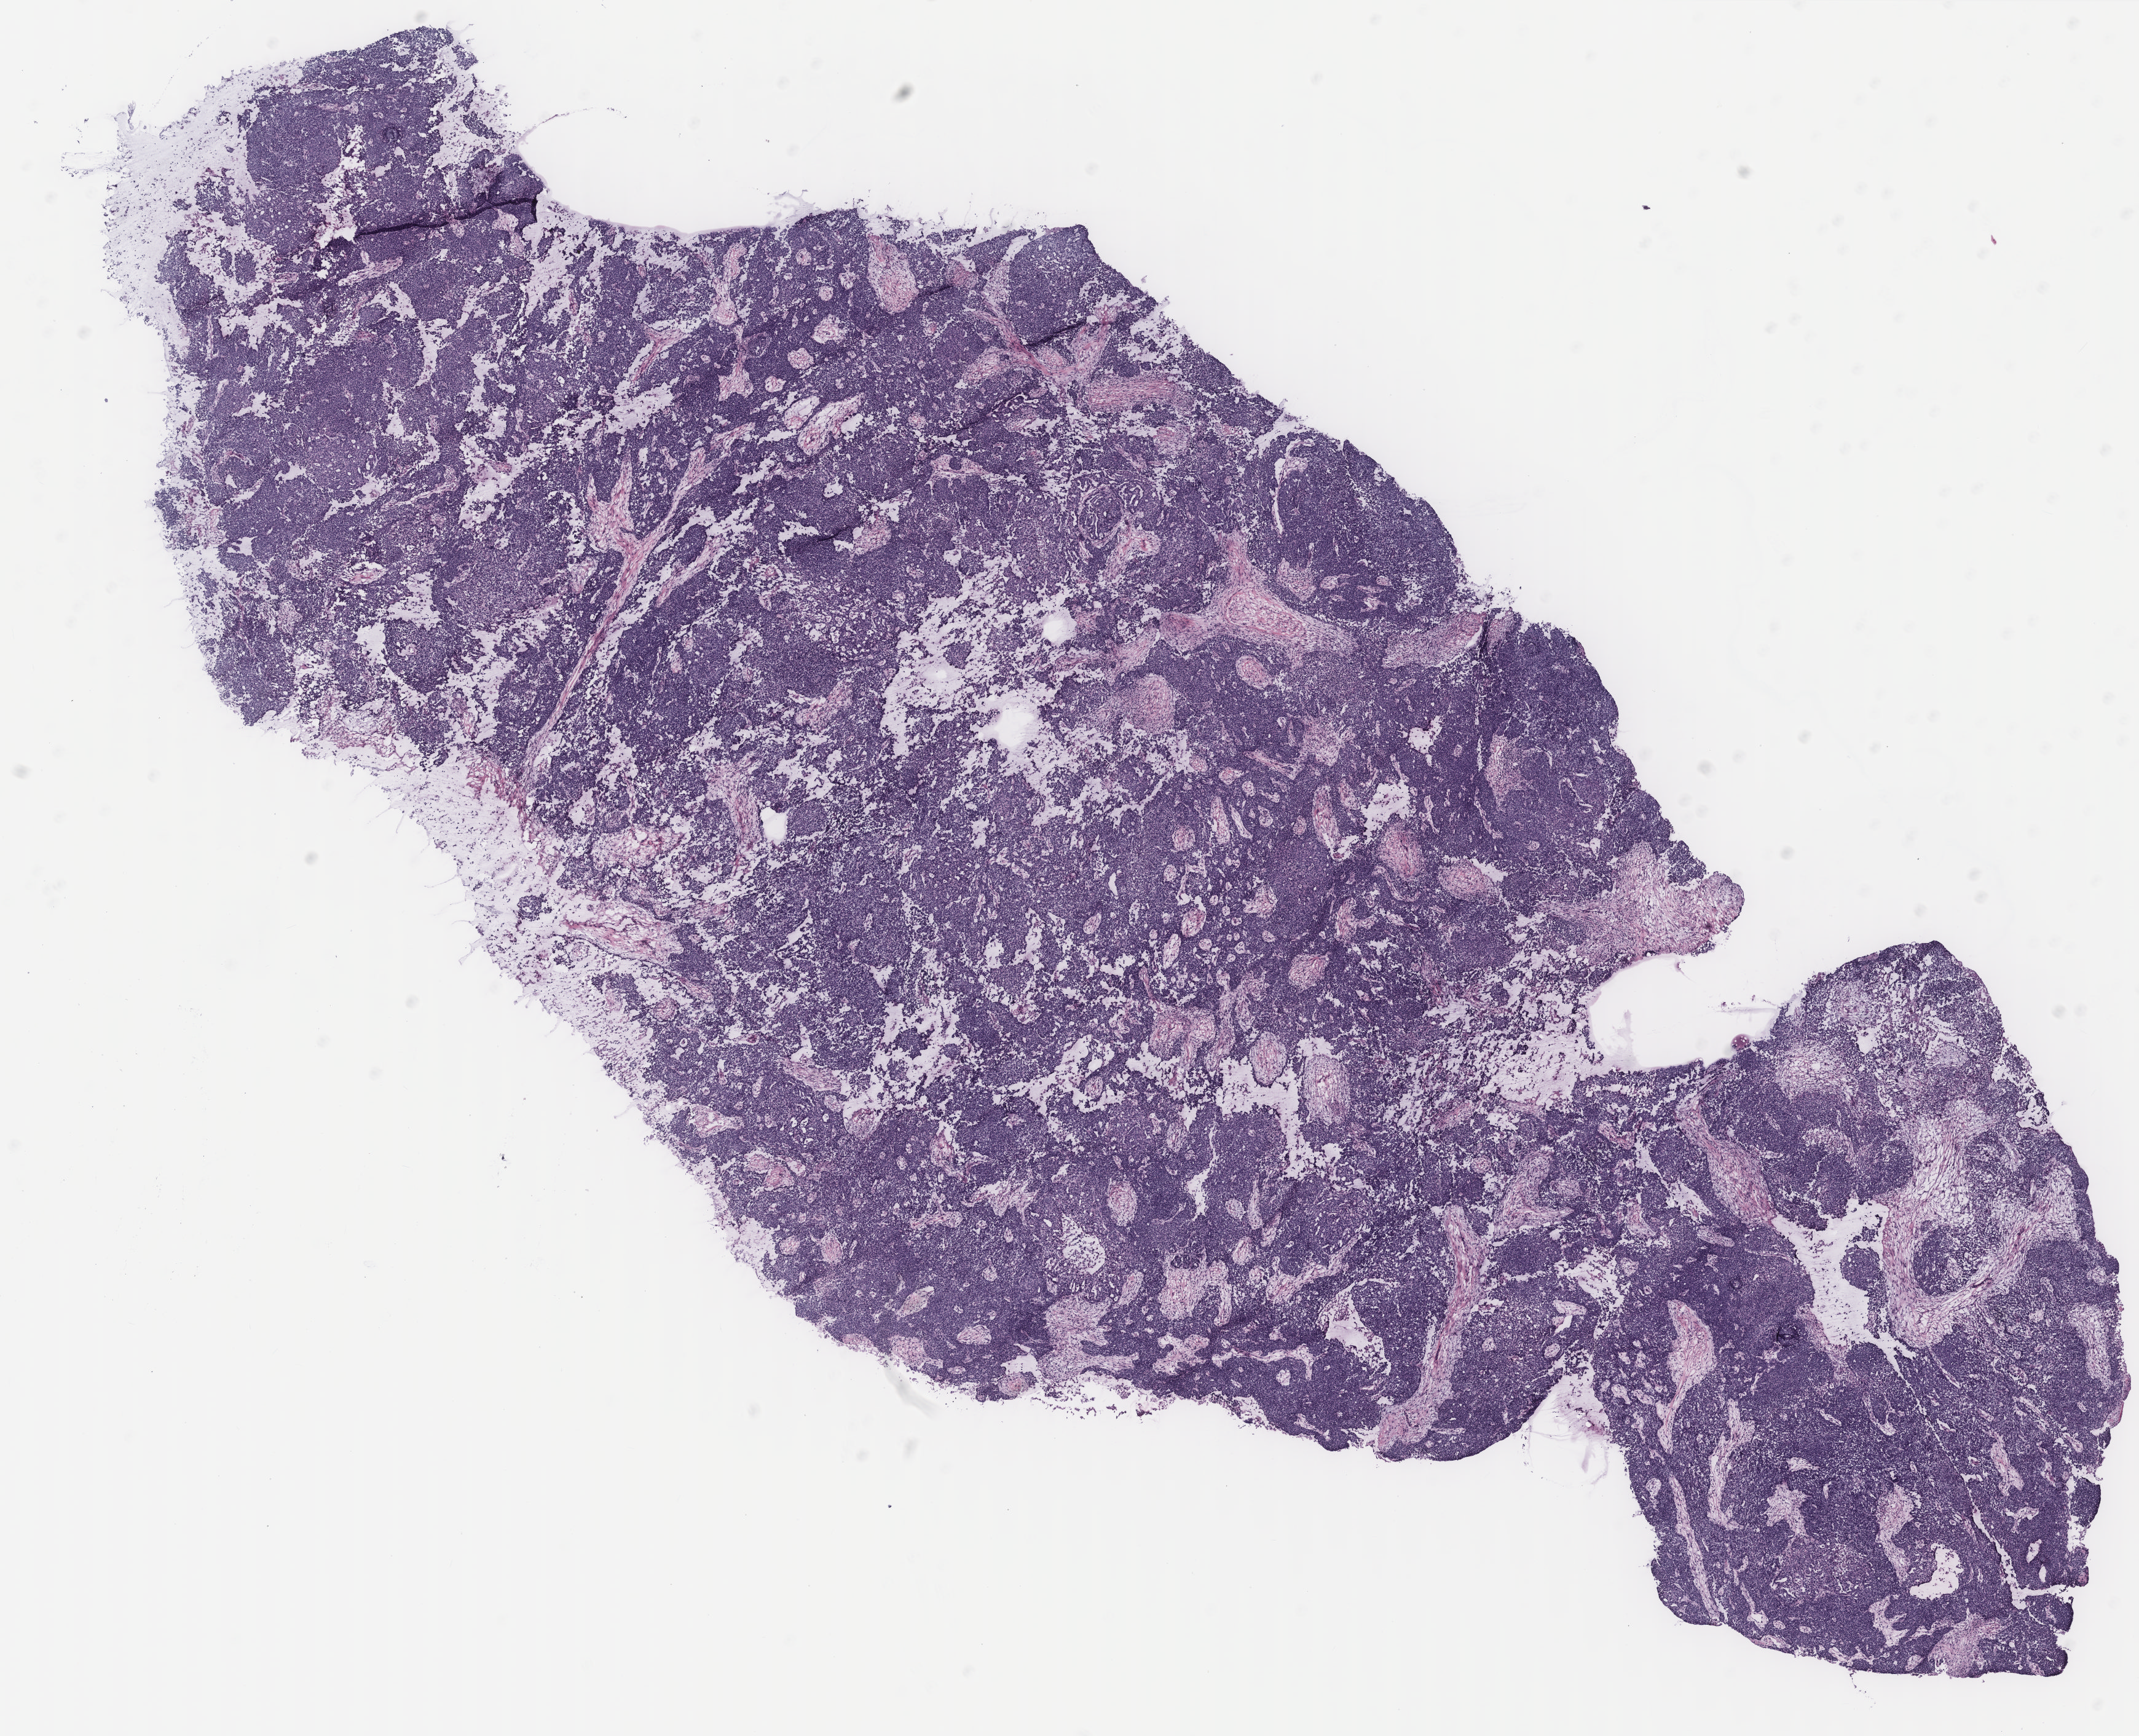
Digitized Hematoxylin and eosin (H&E) stained tissue section (whole slide) — low-resolution overview of the scanned area, about 13.9 x 11.3 mm. Ovary, tumour tissue. Female, 54 y/o.
Histologic diagnosis: Serous adenocarcinoma, NOS (peritoneum, NOS).